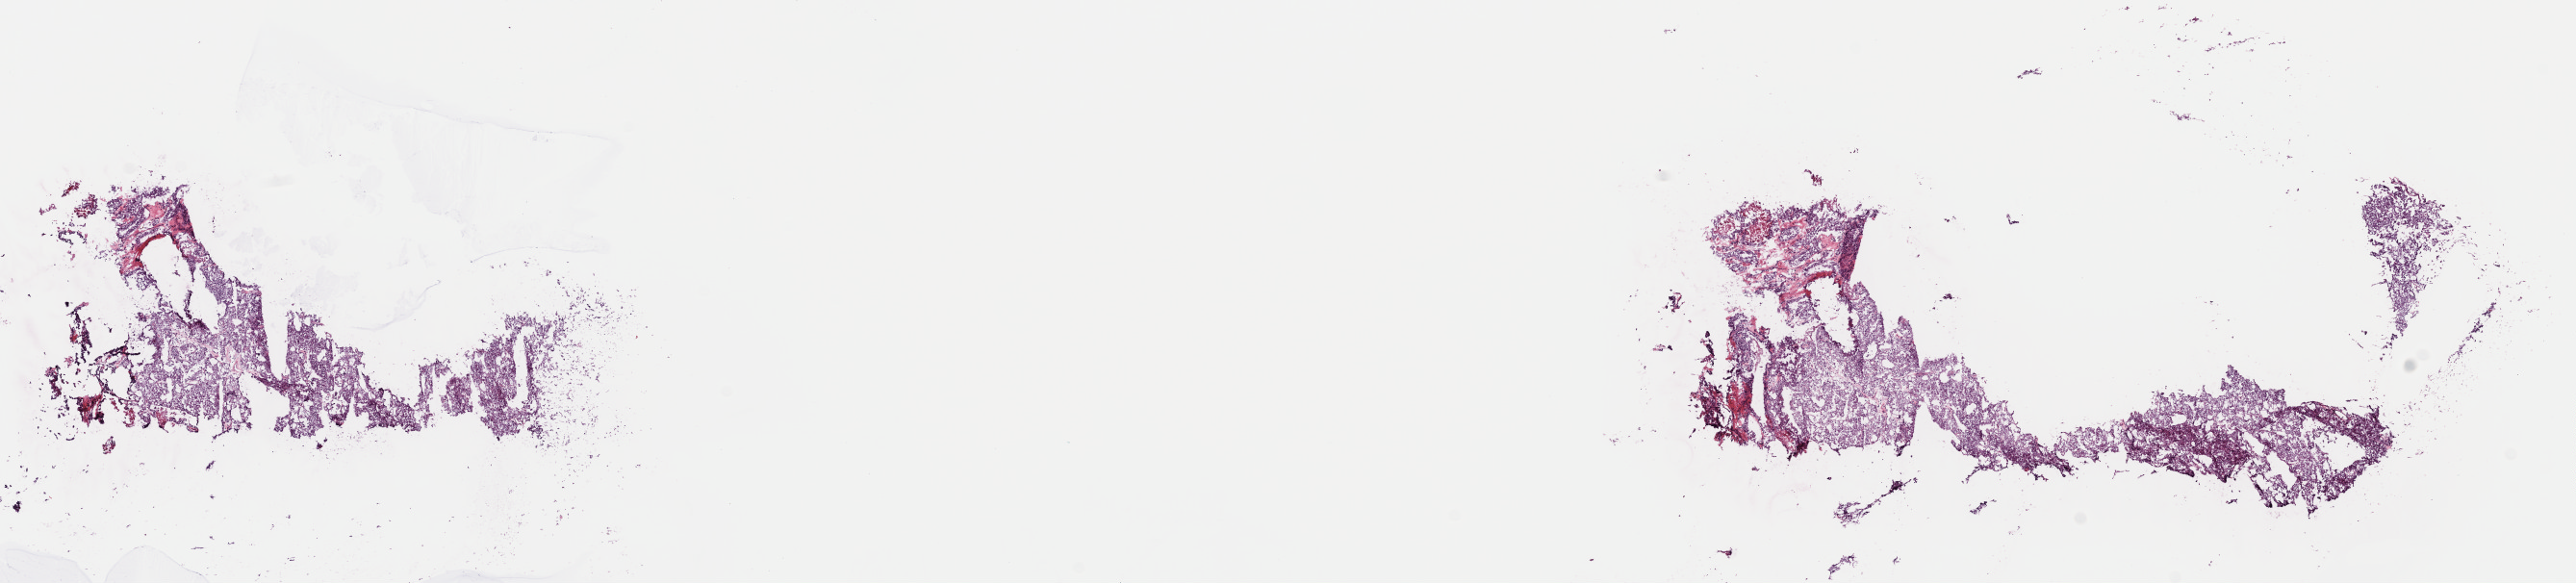
Digitized H&E-stained tissue section (whole slide), whole scanned area (about 21.1 x 4.8 mm) shown as a low-resolution overview, frozen section from the top of the tissue portion, primary tumour sample from the kidney. Female patient; age at initial diagnosis 42 years. Slide review estimates, as recorded: tumour cells 90%, tumour nuclei 95%, normal cells 0%, stromal cells 10%, necrosis 0%. Infiltration values recorded for this section: lymphocyte infiltration 0%, monocyte infiltration 0%, neutrophil infiltration 0%.
Pathologic diagnosis: Renal cell carcinoma, chromophobe type. Laterality: left. AJCC pathologic stage: I (7th edition).